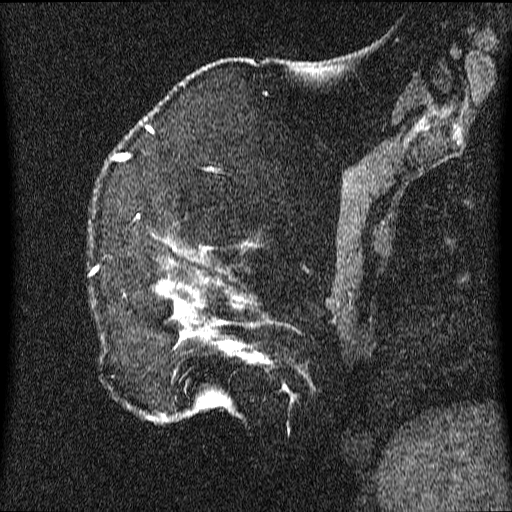
Breast MRI (dynamic contrast-enhanced), one sagittal slice; position 13 of 64 along the scan axis; dynamic contrast-enhanced series, image 2 of 3 at this slice position (ordered by acquisition); 1.5 T; TE 4.2 ms, TR 9.1 ms; 2.2 mm slice thickness; 512 × 512 image matrix, field of view 180 × 180 mm. Female patient, age 52 years.
Outlined on this slice (semi-automatically segmented with operator editing):
- analysis volume of interest (the breast-tissue region the enhancement analysis was run in; not a lesion): bounding box <92,204,347,424> (left, top, right, bottom; pixels)
- tumour enhancement mask (voxels above the 70 % enhancement threshold inside the analysis volume of interest): <158,249,270,418>